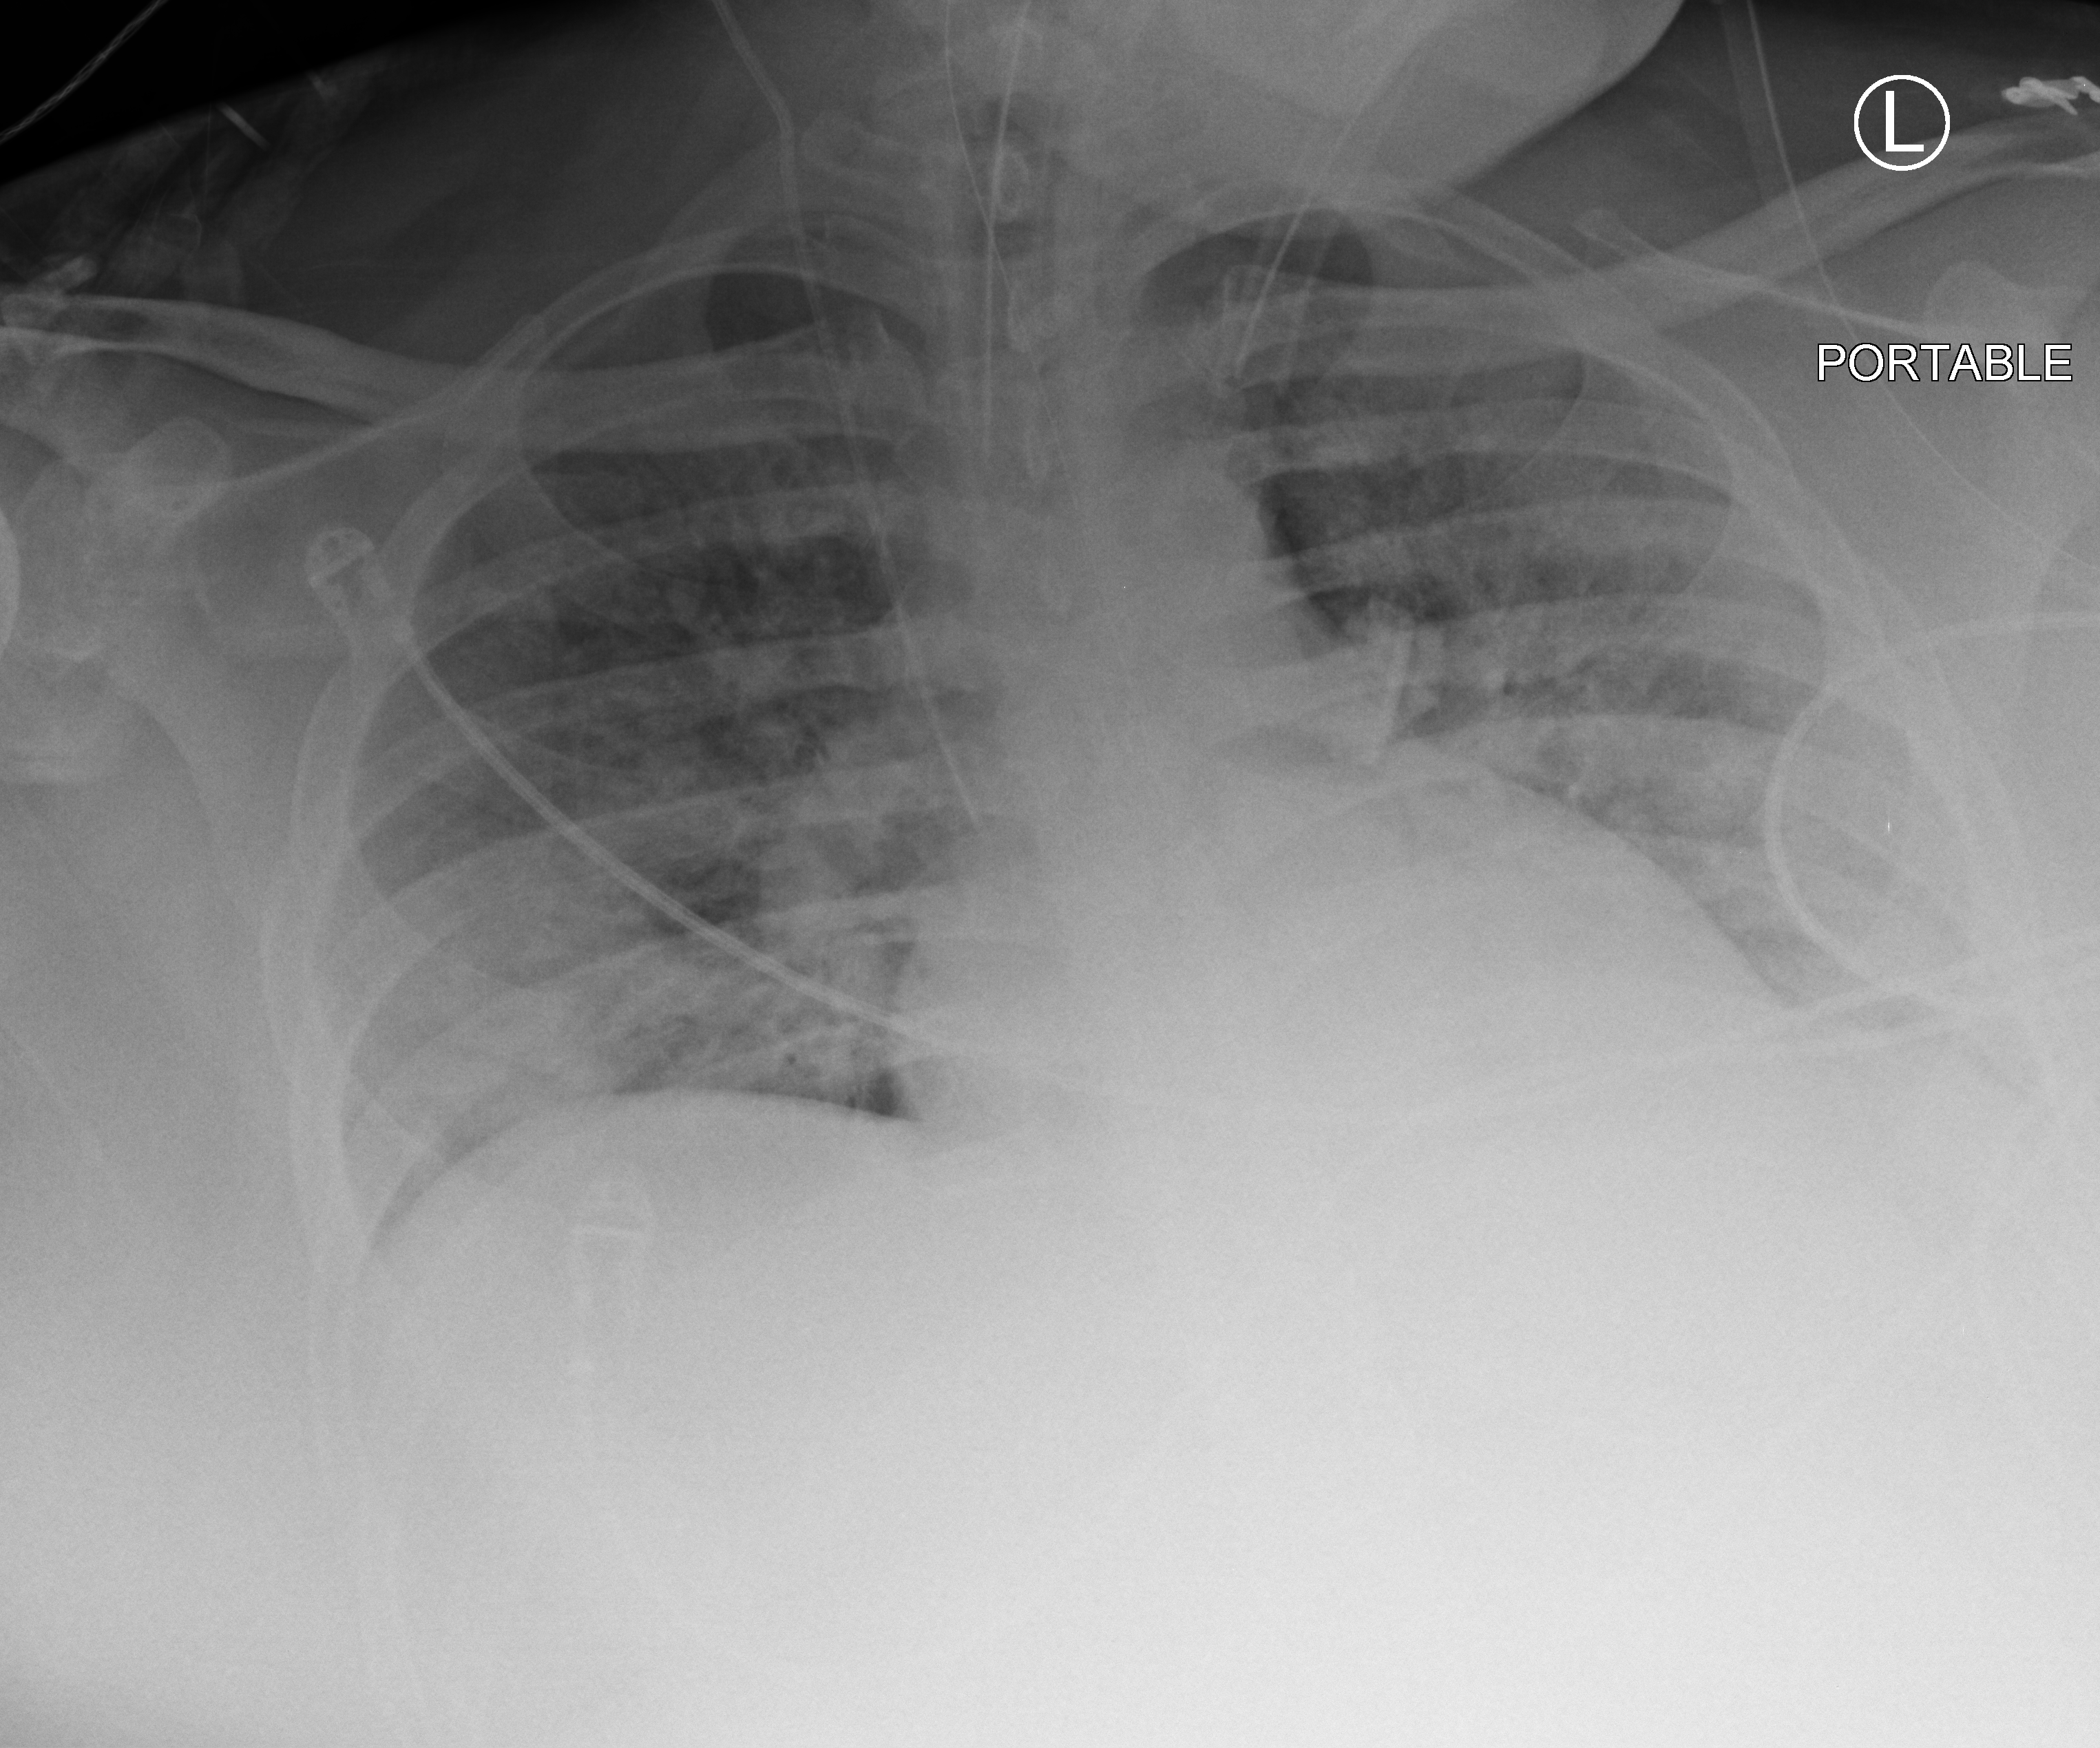
Bedside chest radiograph (computed radiography). Patient hospitalised with COVID-19; male, aged 18–59 years.
From the hospital-stay record, not from the radiograph (when in the stay this image was taken is not recorded):
- length of hospital stay: 69 days
- mechanically ventilated during this hospital stay: yes
- COPD (admission record): yes